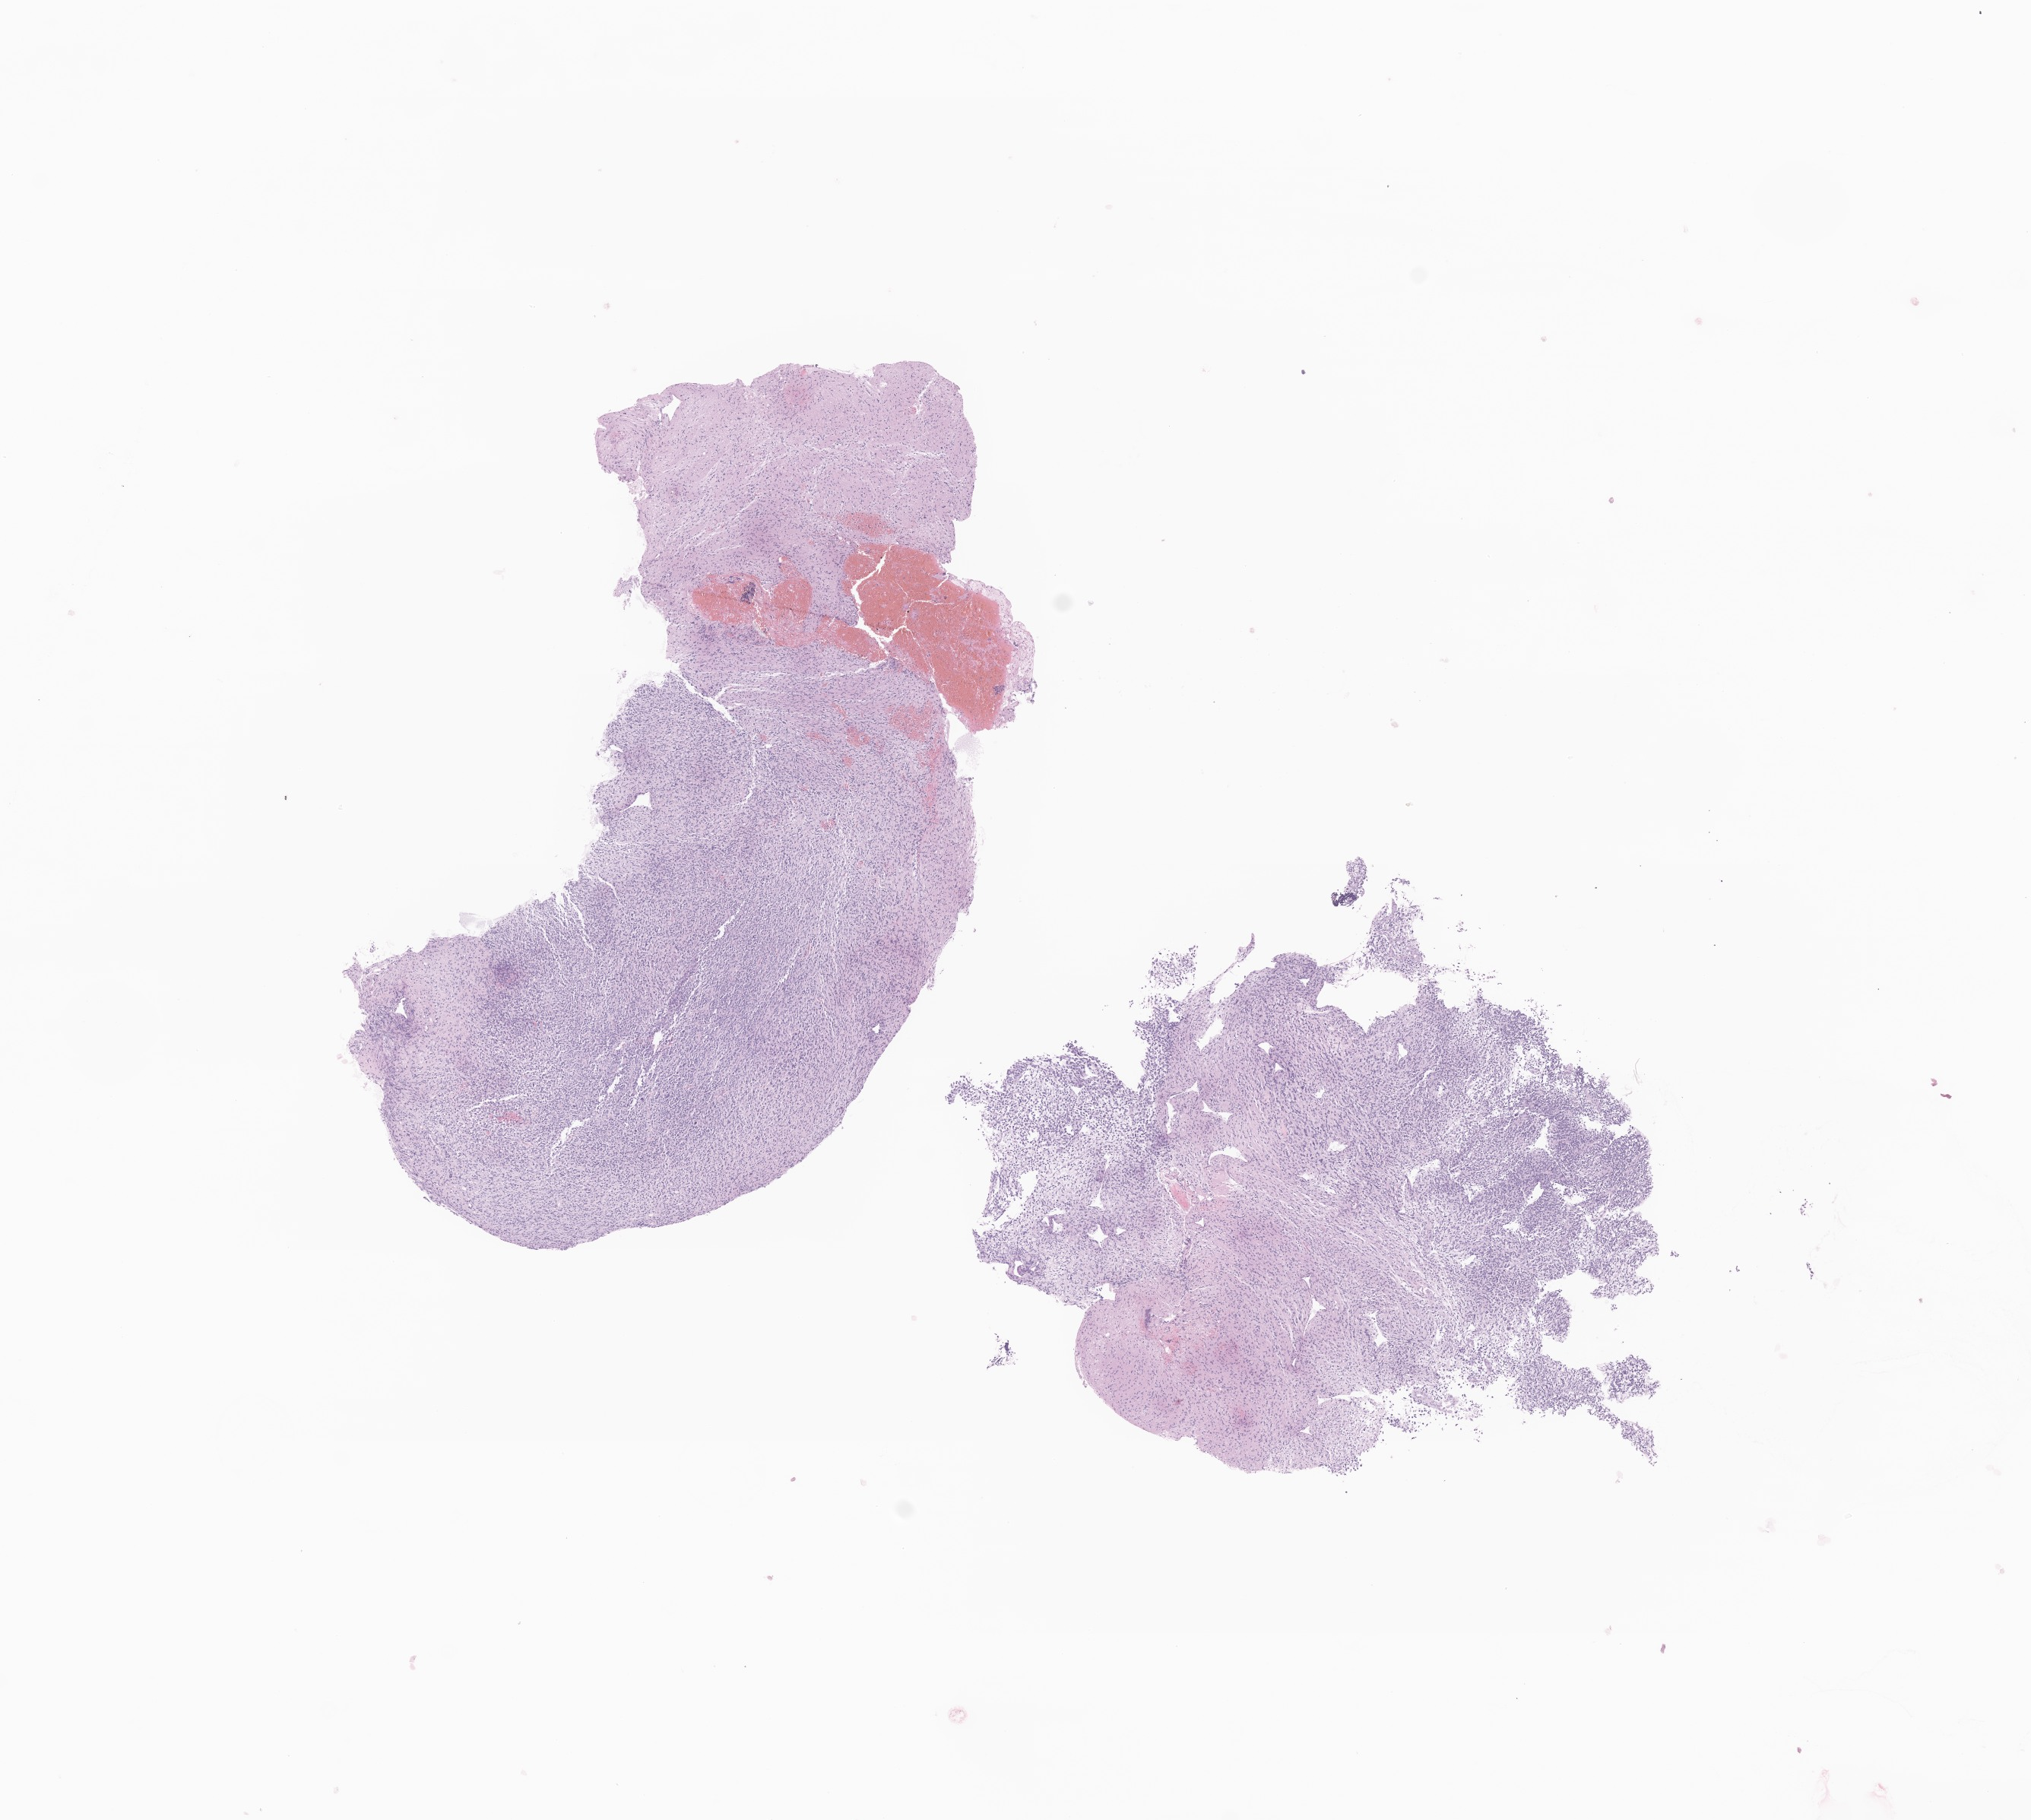
Whole-slide image, H&E stain of tumor tissue from the brain — low-resolution overview of the scanned area, about 11.2 x 10.0 mm; FFPE section. Patient: male, age 77 months (6 years 5 months).
Diagnosis (ICD-O-3 morphology term): Glioma, malignant.